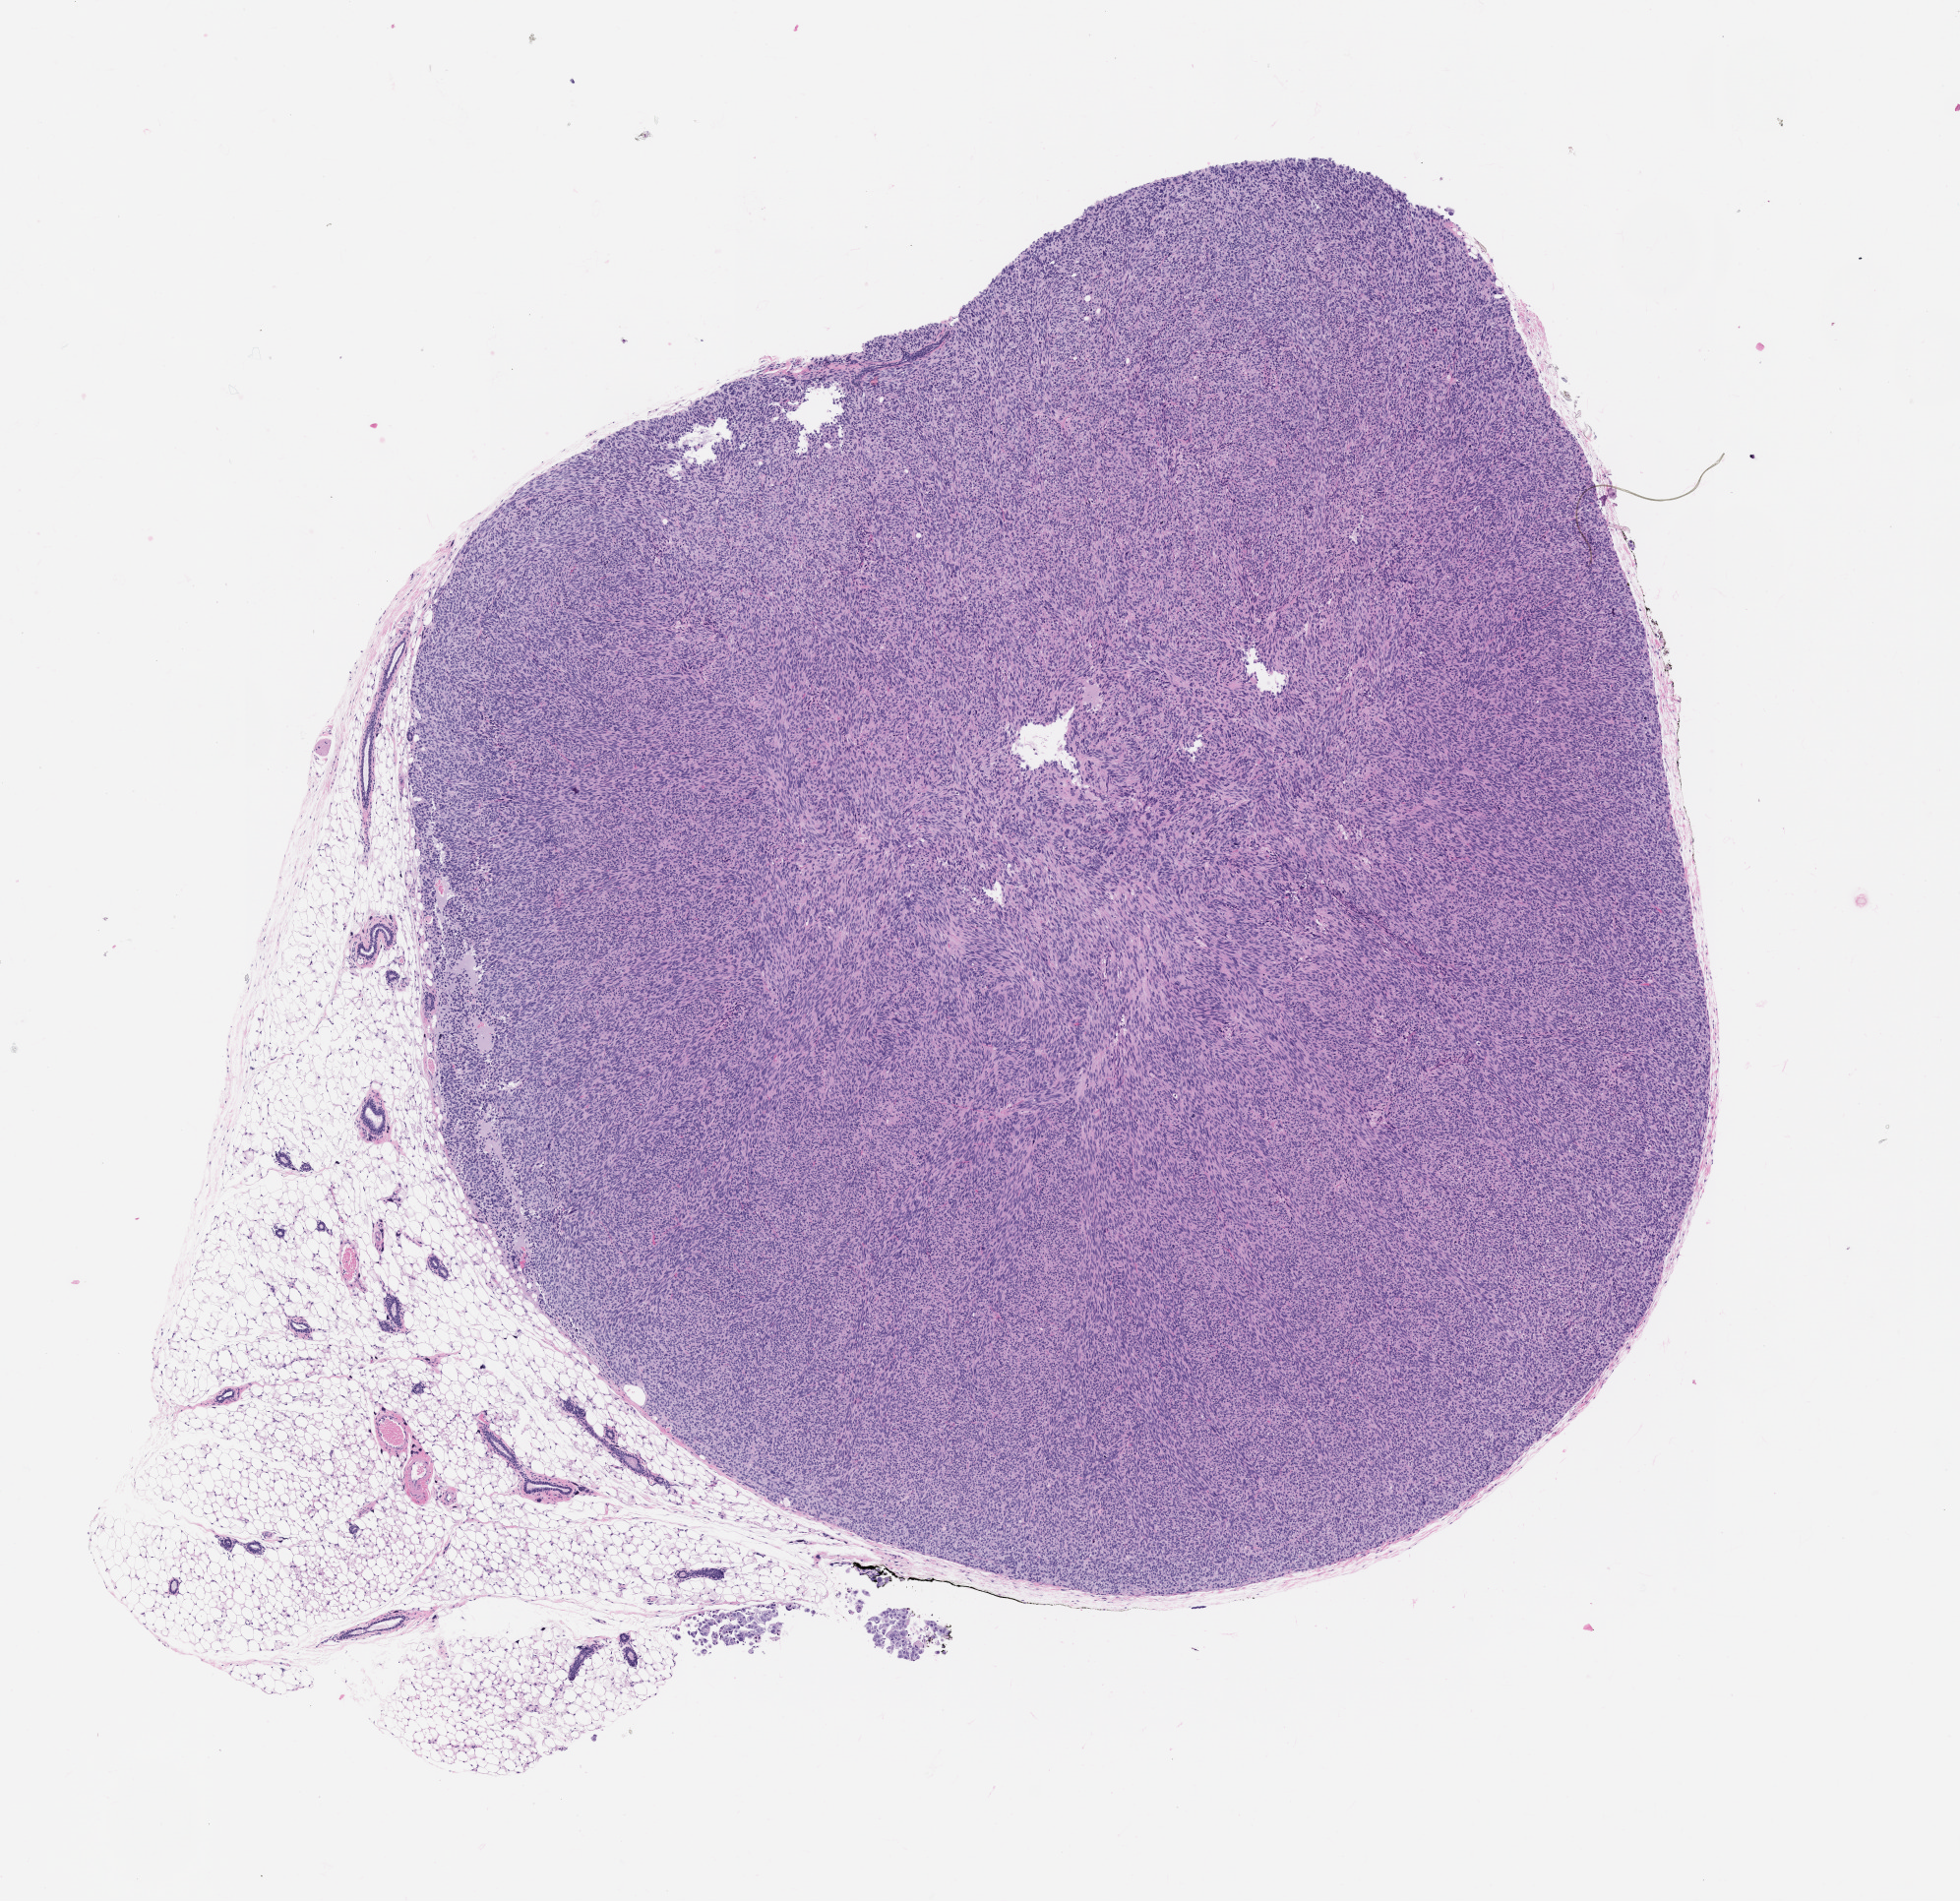
H&E whole-slide image of a patient-derived xenograft (PDX) tumor grown in a mouse, passage 3, whole scanned area (about 8.0 x 7.8 mm) shown as a low-resolution overview. Formalin-fixed, paraffin-embedded (FFPE) tissue. Originating tumor site category: uterus.
Originating patient diagnosis: Leiomyosarcoma.